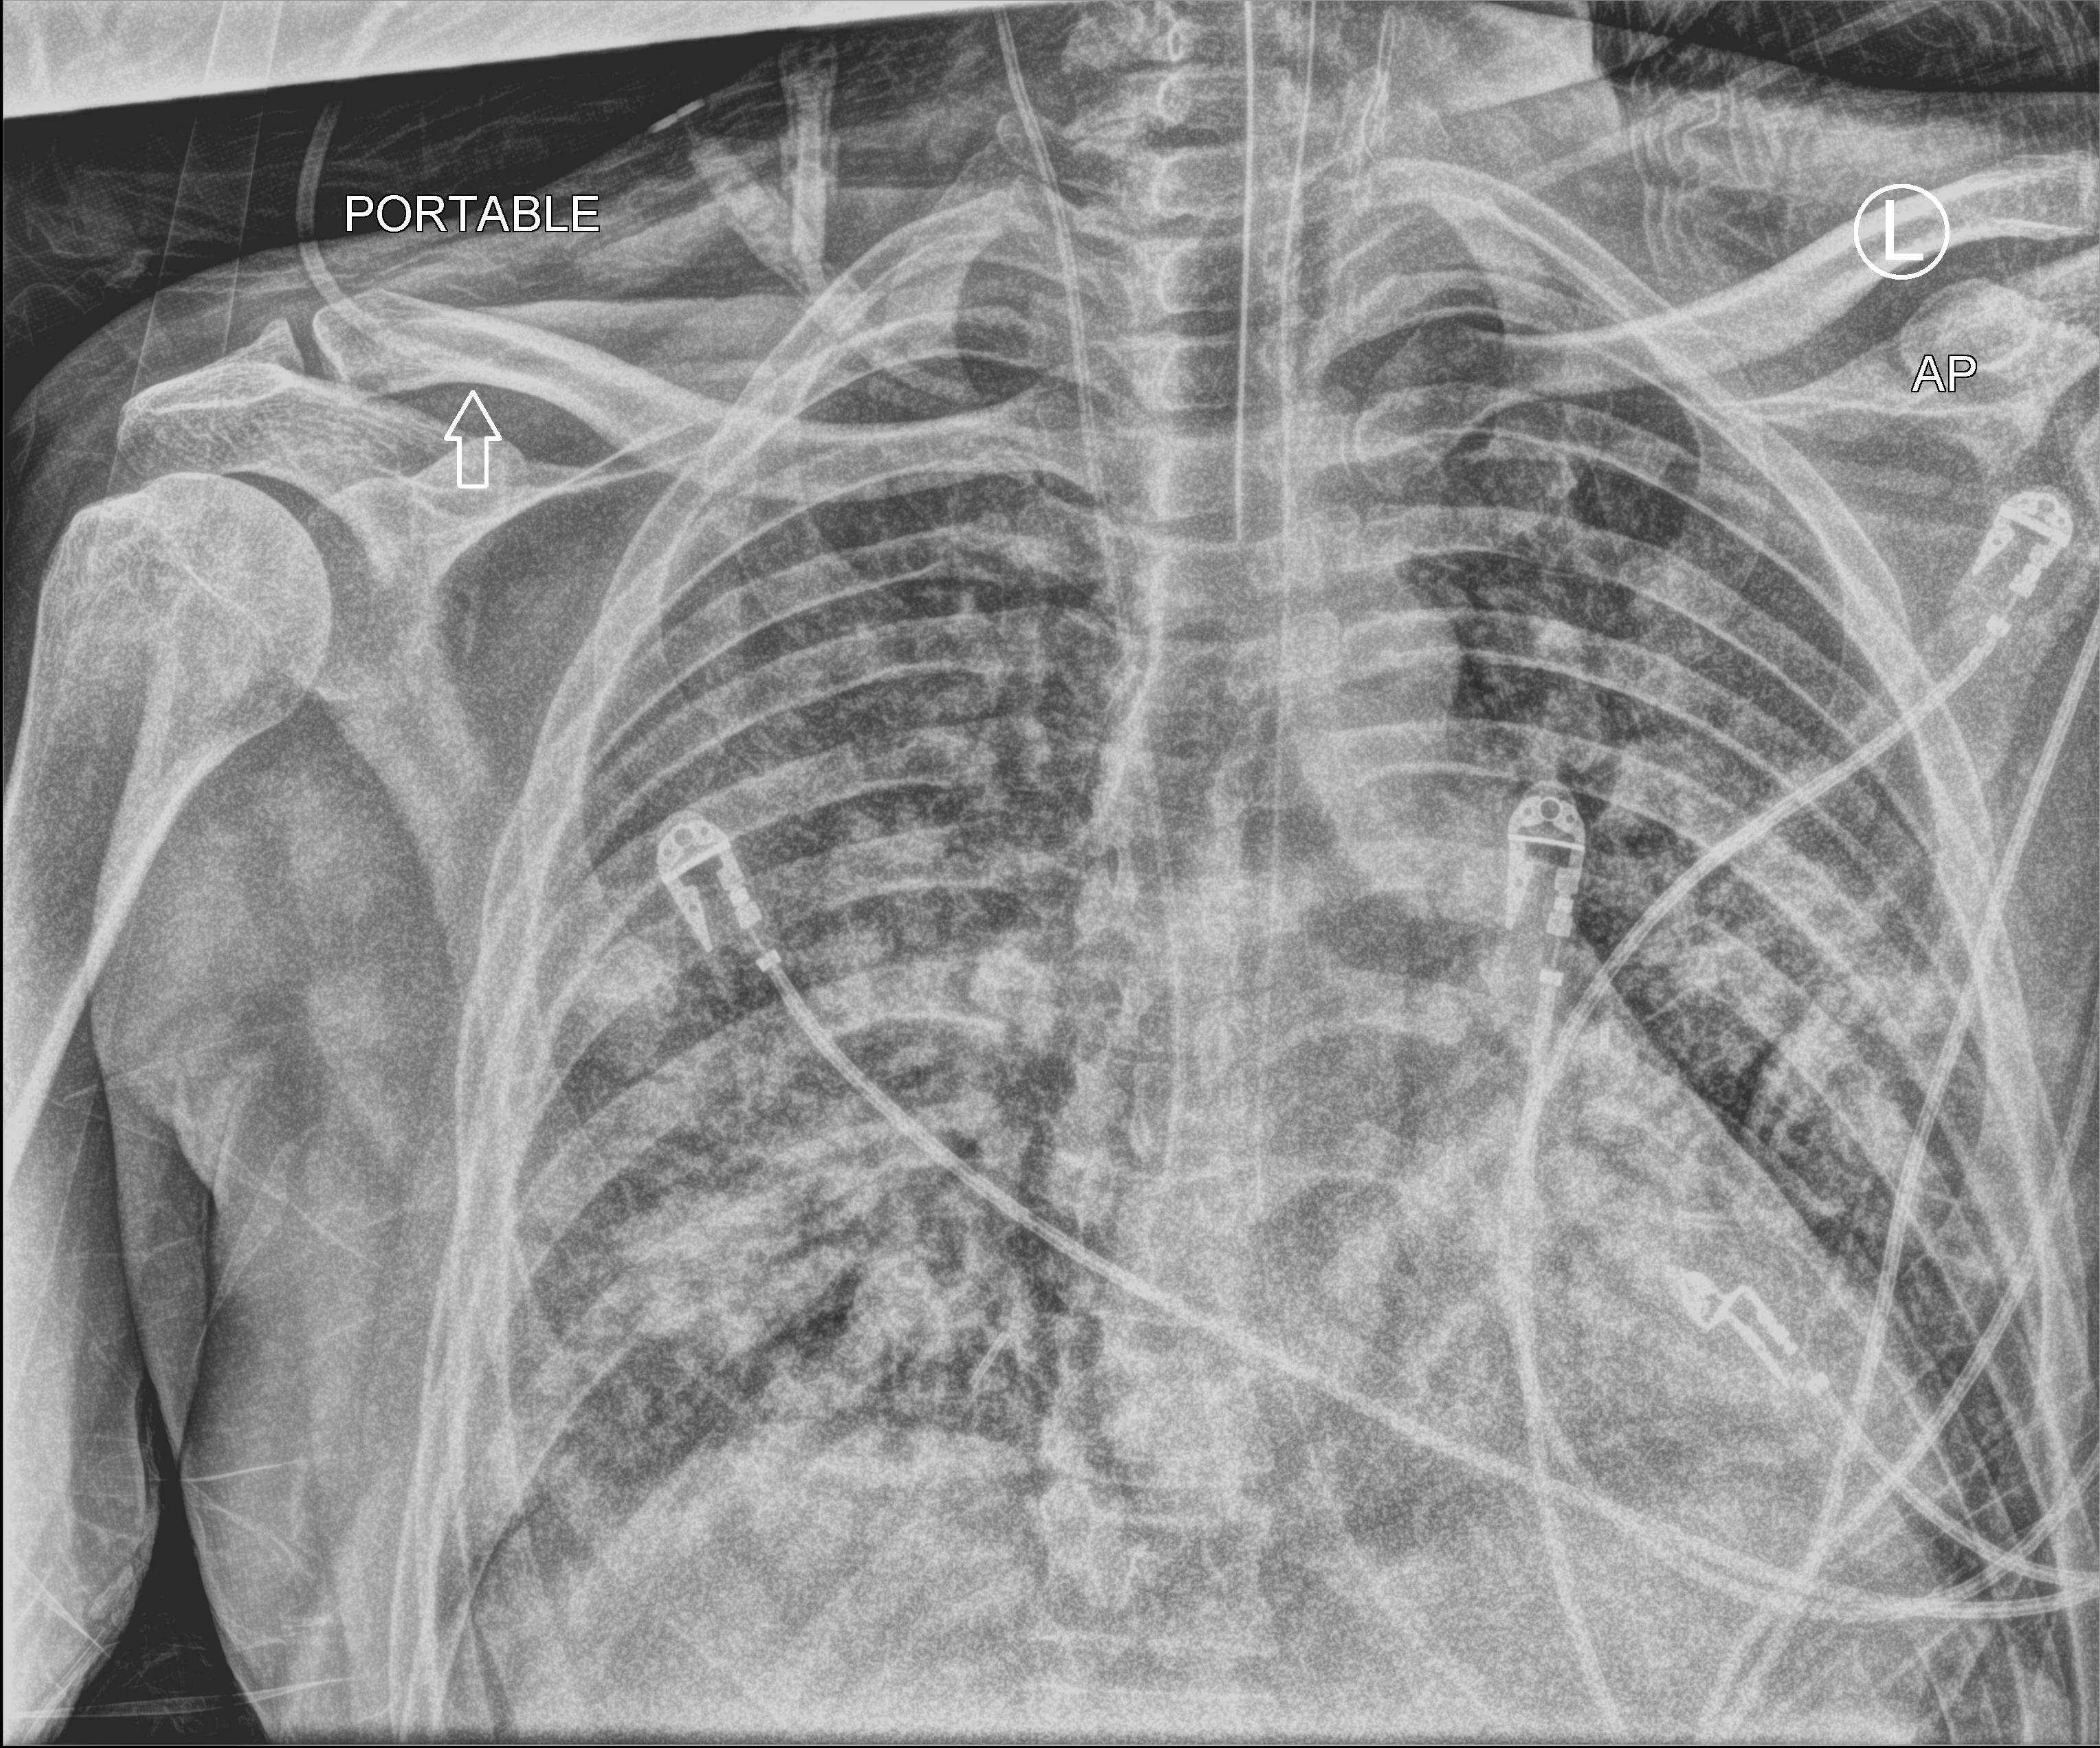
Portable chest radiograph; anteroposterior (AP) projection. Male patient hospitalised with COVID-19, age 18–59 years.
Admission-level facts for this patient (not findings on this image; timing relative to this image not recorded):
- diabetes (admission record): no
- mechanically ventilated during this hospital stay: yes
- admitted to intensive care during this hospital stay: yes